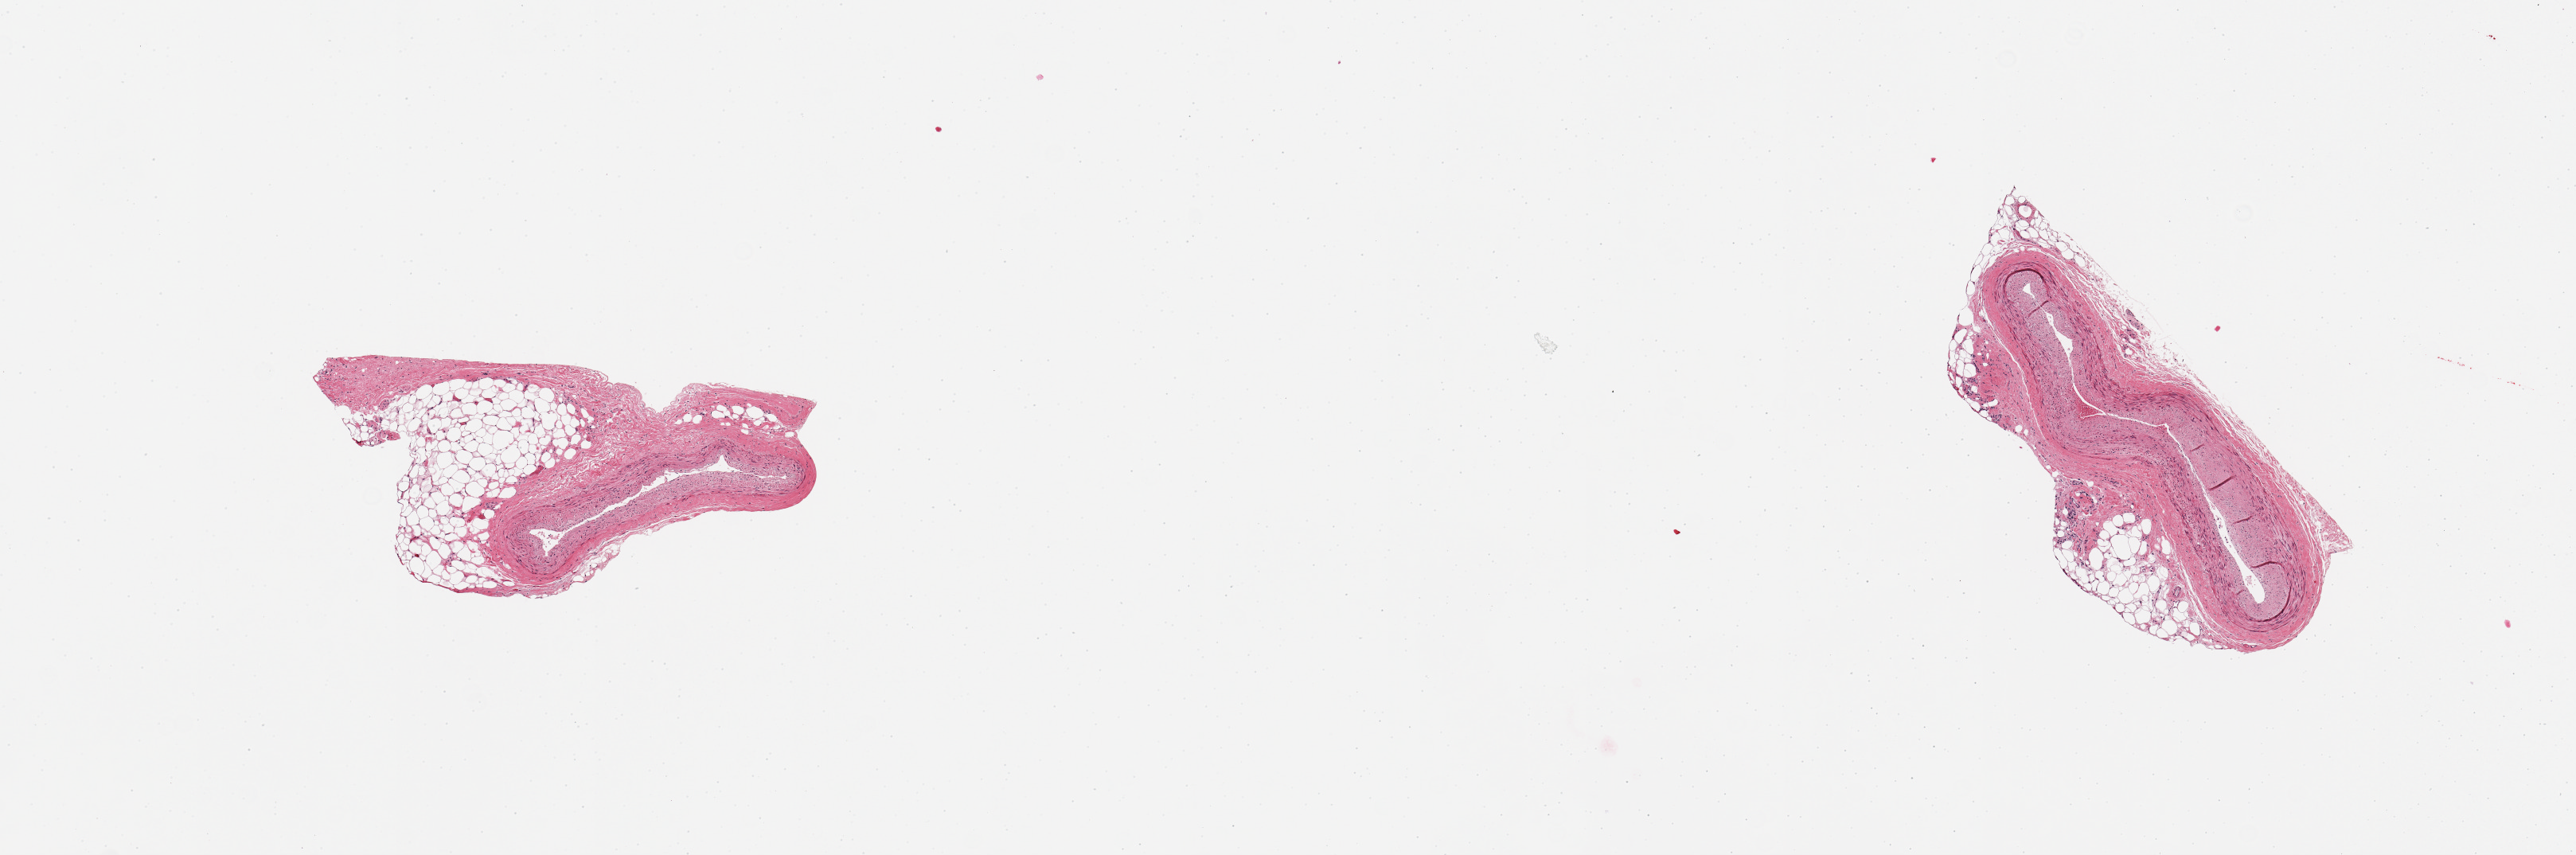
Digitized haematoxylin and eosin-stained section, brightfield — shown as a low-resolution overview of the whole scanned area (about 12.8 x 4.2 mm, acquisition: 20x scan), PAXgene-fixed paraffin-embedded (PFPE) section, section of coronary artery (target tissue), donor tissue sample. Male donor.
Reviewer comment on this tissue sample: 2 pieces, minimal atherosis, adherent fat/connective tissues up to ~1mm.